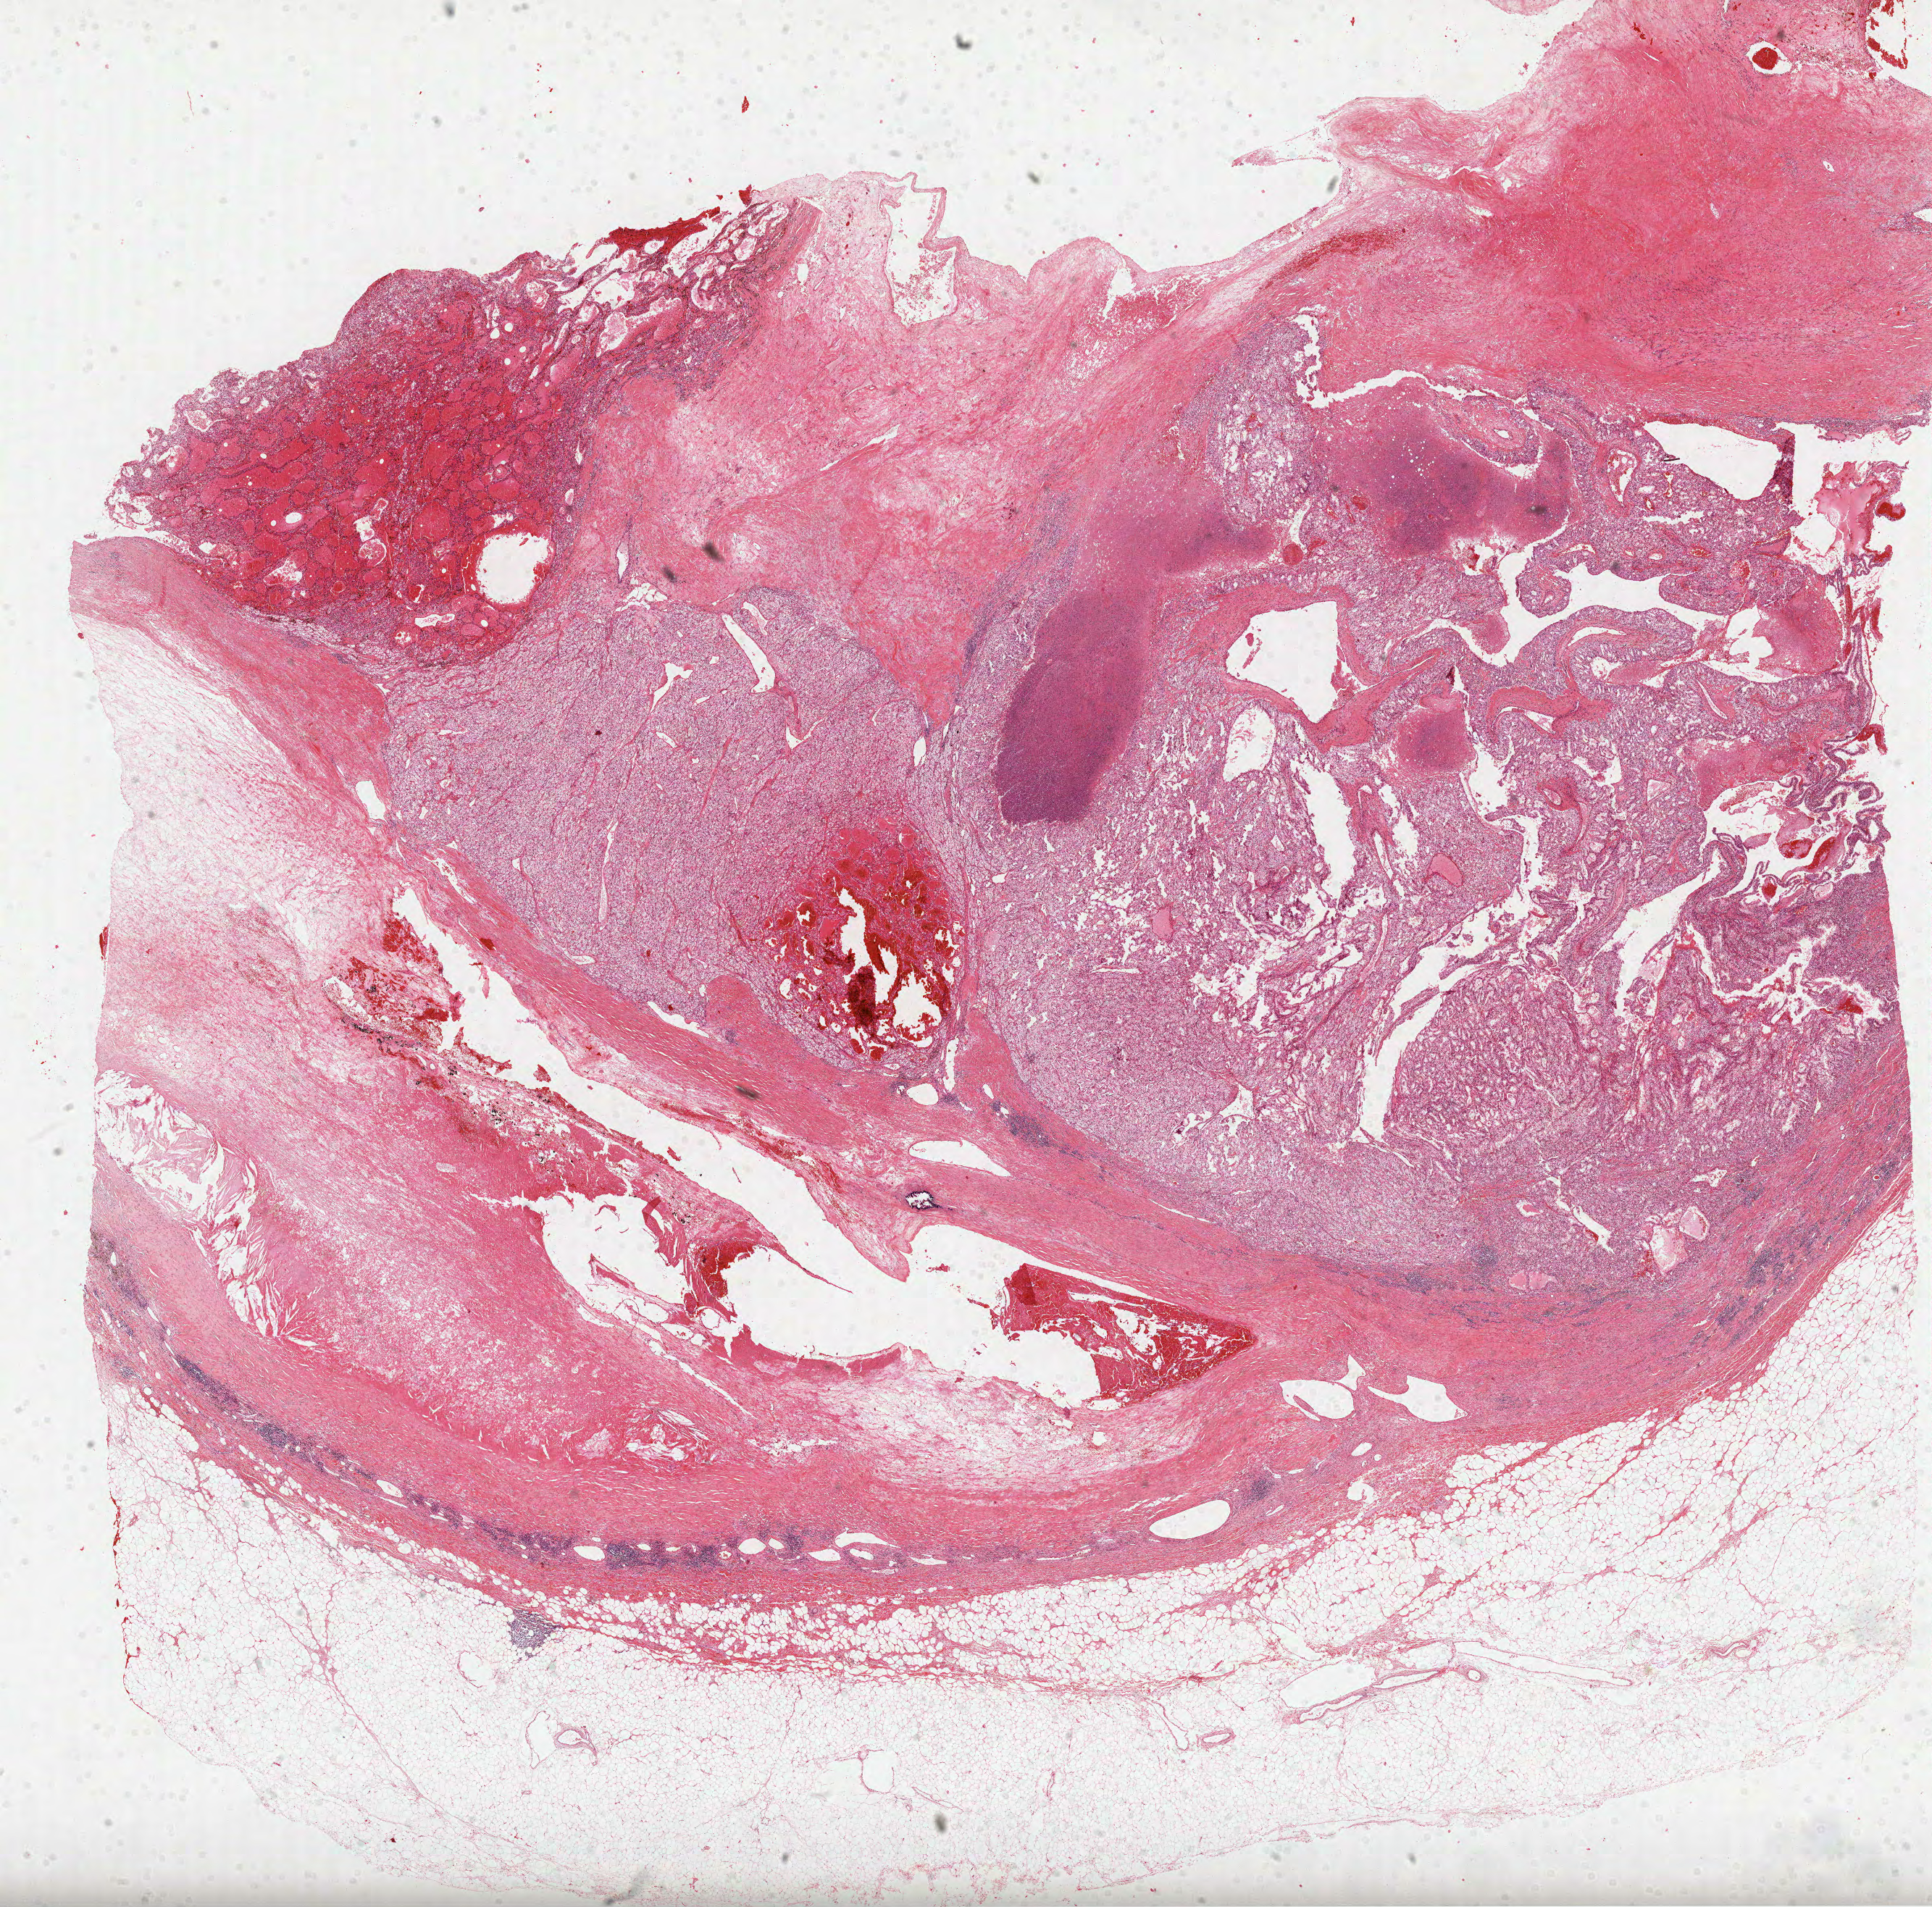
Whole-slide histology image, H&E-stained, low-resolution overview of the scanned area, about 21.5 x 21.2 mm (slide scanned at 40x), formalin-fixed paraffin-embedded (FFPE) diagnostic section, sample: primary tumour, kidney. Male, age 73 years at initial diagnosis. Histologic grade: G3 (poorly differentiated).
• laterality: left
• pathologic diagnosis: Clear cell adenocarcinoma, NOS
• AJCC pathologic stage: I (6th edition)
• TNM: T1b N0 M0